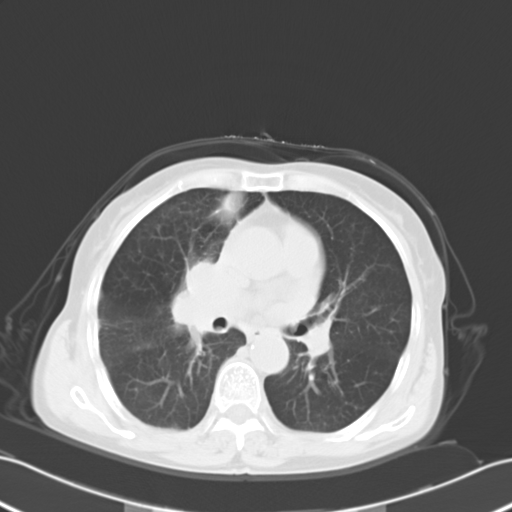
Chest CT, one axial slice. Slice 15 of 27 in the series (ordered by position). Reconstruction kernel B40f. 120 kVp. Lung window (W 1500 / L -600 HU). 10 mm slice thickness. 512 × 512 image matrix. Patient: female, 67 years. From the clinical record (not read from this slice): clinical TNM (as recorded): T2a N3 M0.
Structures marked on this image (bounding box drawn by a radiologist):
- lung tumour (recorded histology: small cell carcinoma): bounding box [x1, y1, x2, y2] px = [169, 255, 222, 339]